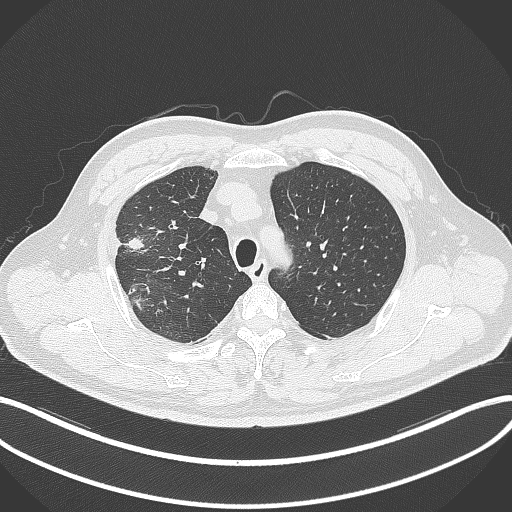
Chest CT, one axial slice. Reconstruction kernel B70f. 120 kVp. Lung window (W 1500 / L -600 HU). 1 mm slice thickness. 512 × 512 image matrix, field of view 400 × 400 mm. Male patient, age 55 years. From the clinical record (not read from this slice): clinical TNM (as recorded): T3 N2 M1.
Outlined on this slice (bounding box drawn by a radiologist):
- lung tumour (recorded histology: adenocarcinoma): bounding box [x1, y1, x2, y2] px = [123, 232, 149, 254]